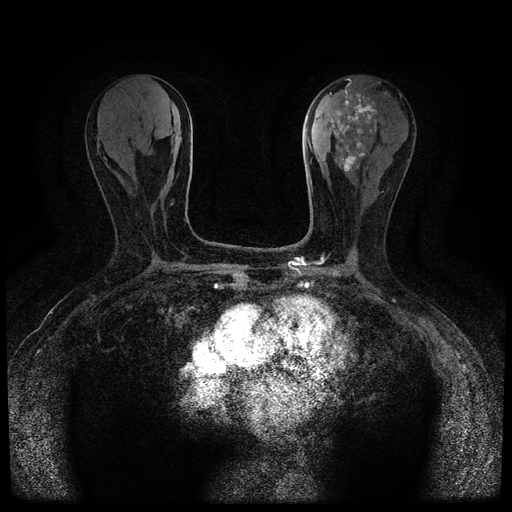
Breast MRI (dynamic contrast-enhanced, multi-phase), one axial slice. Slice 37 of 116 in the series (ordered by position). Dynamic contrast-enhanced series, time point 2 of 5 at this slice position (early post-contrast). 1.5 T. TE 2.7 ms, TR 5.4 ms. 2 mm slice thickness. 512 × 512 image matrix. Female patient, age 80 years.
Outlined on this slice (semi-automatic segmentation, software-assisted and operator-edited):
- breast lesion (labelled 'tumour' in the annotation; benign lesions carry a separate 'benign' label): bounding box <331,94,377,172> (left, top, right, bottom; pixels)